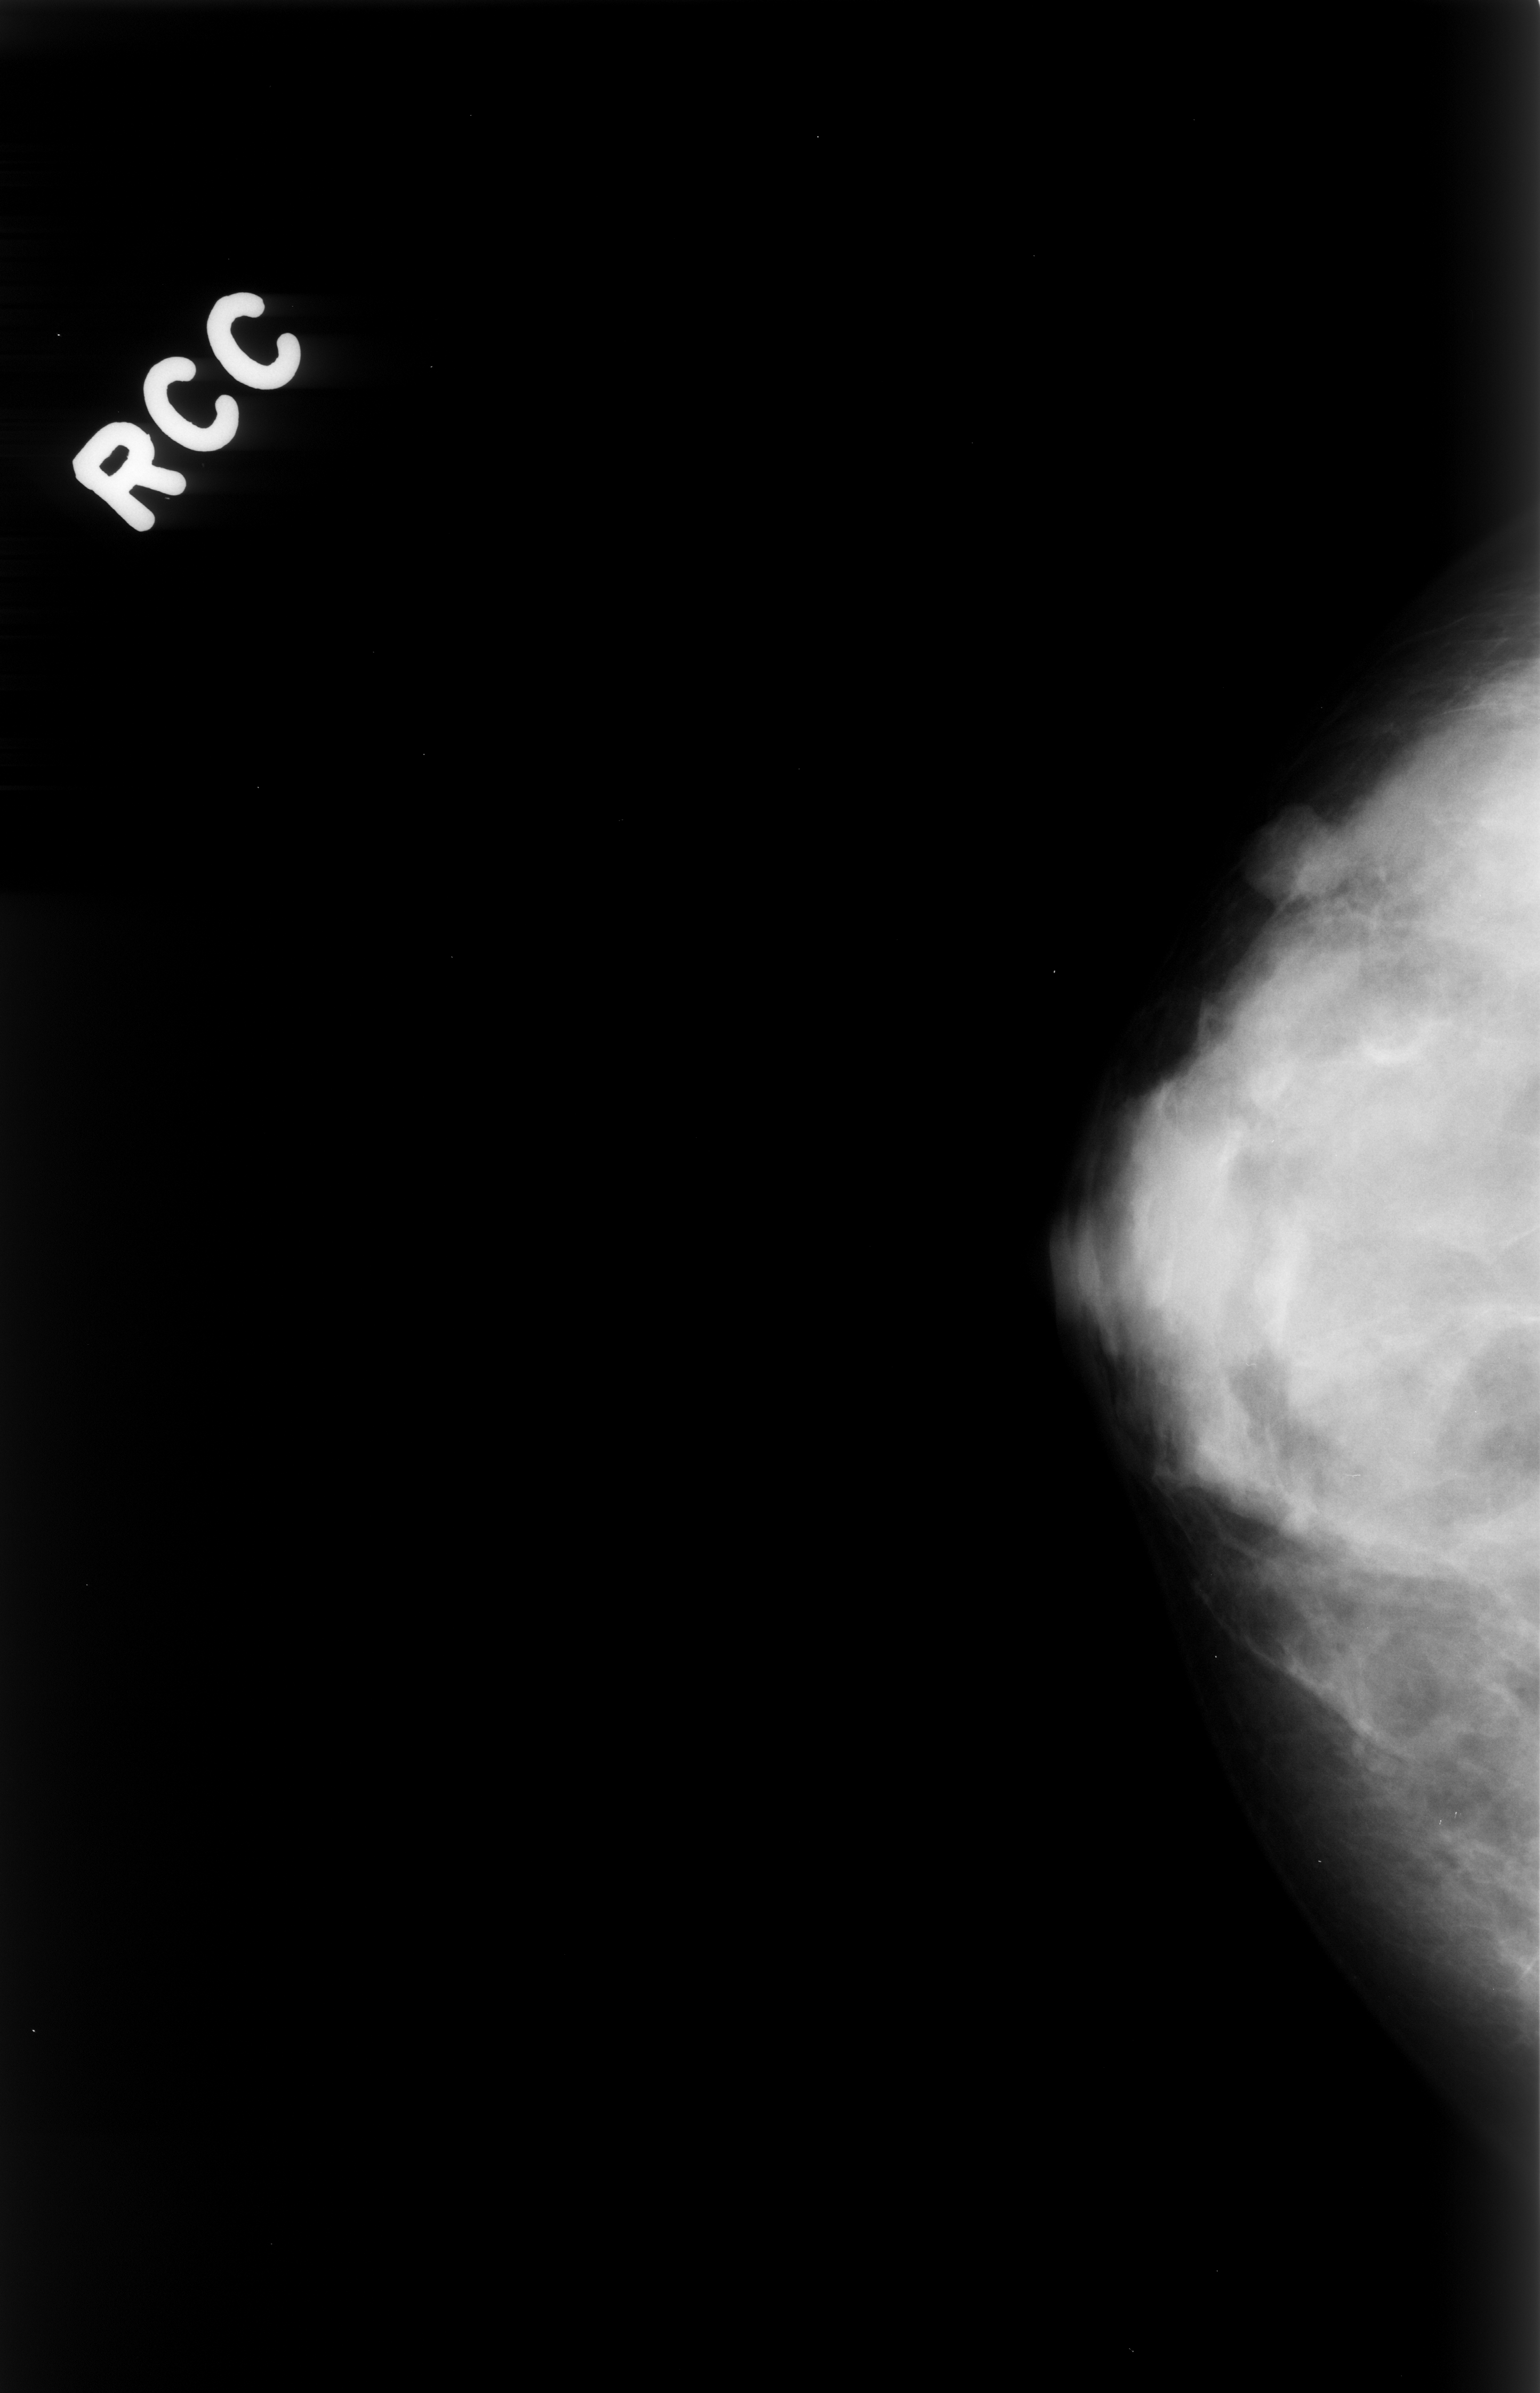
Mammogram (digitized film). Right breast. Craniocaudal (CC) view. Breast composition: heterogeneously dense (BI-RADS density category 3 of 4). 1540 × 2393 image matrix.
Marked abnormalities (boxes around the expert regions of interest):
- mass, shape oval, margins circumscribed; BI-RADS assessment category 4; pathology result (as recorded, not read from the image): benign: bounding box [x1, y1, x2, y2] px = [1238, 800, 1398, 939]